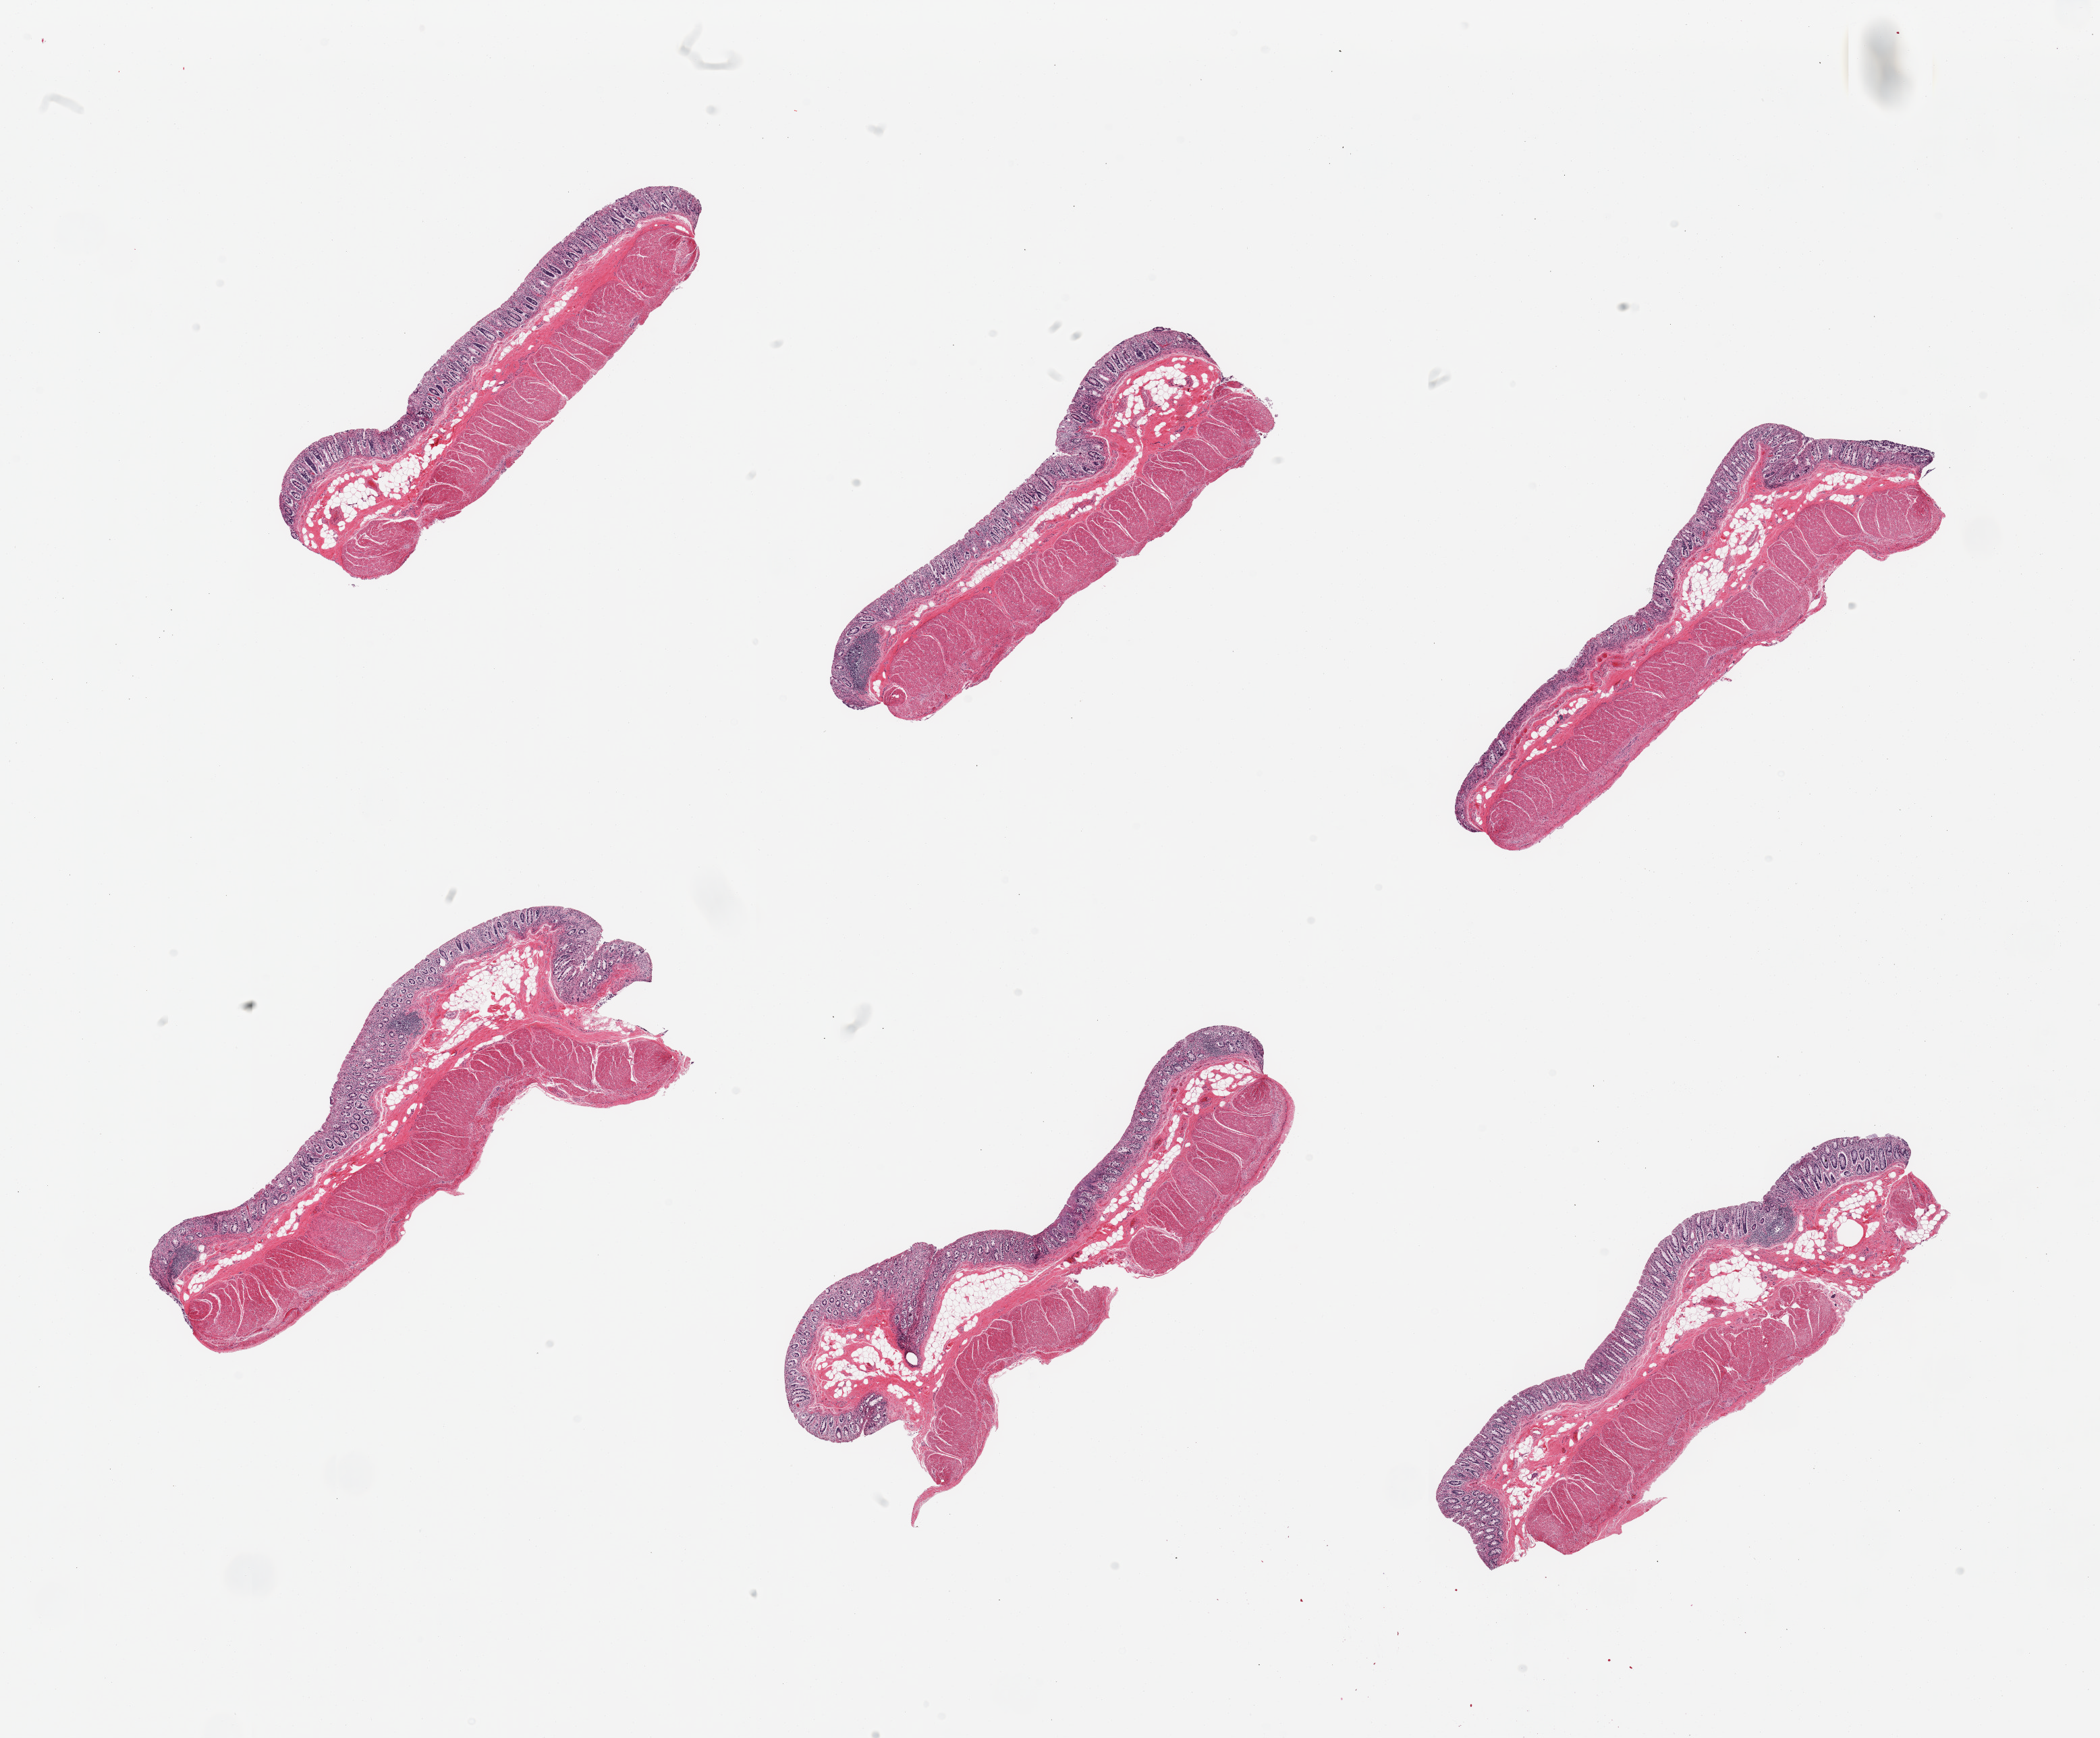
Haematoxylin and eosin whole-slide image — whole scanned area (about 24.6 x 20.4 mm, slide scanned at 20x) shown as a low-resolution overview, PAXgene-fixed paraffin-embedded (PFPE) section, sampled site (target tissue): transverse colon, donor tissue sample. Donor sex: male.
Review note (as recorded): 6 pieces, target mucosa is ~0.35mm, ~25% thickness, moderately advanced autolysis.